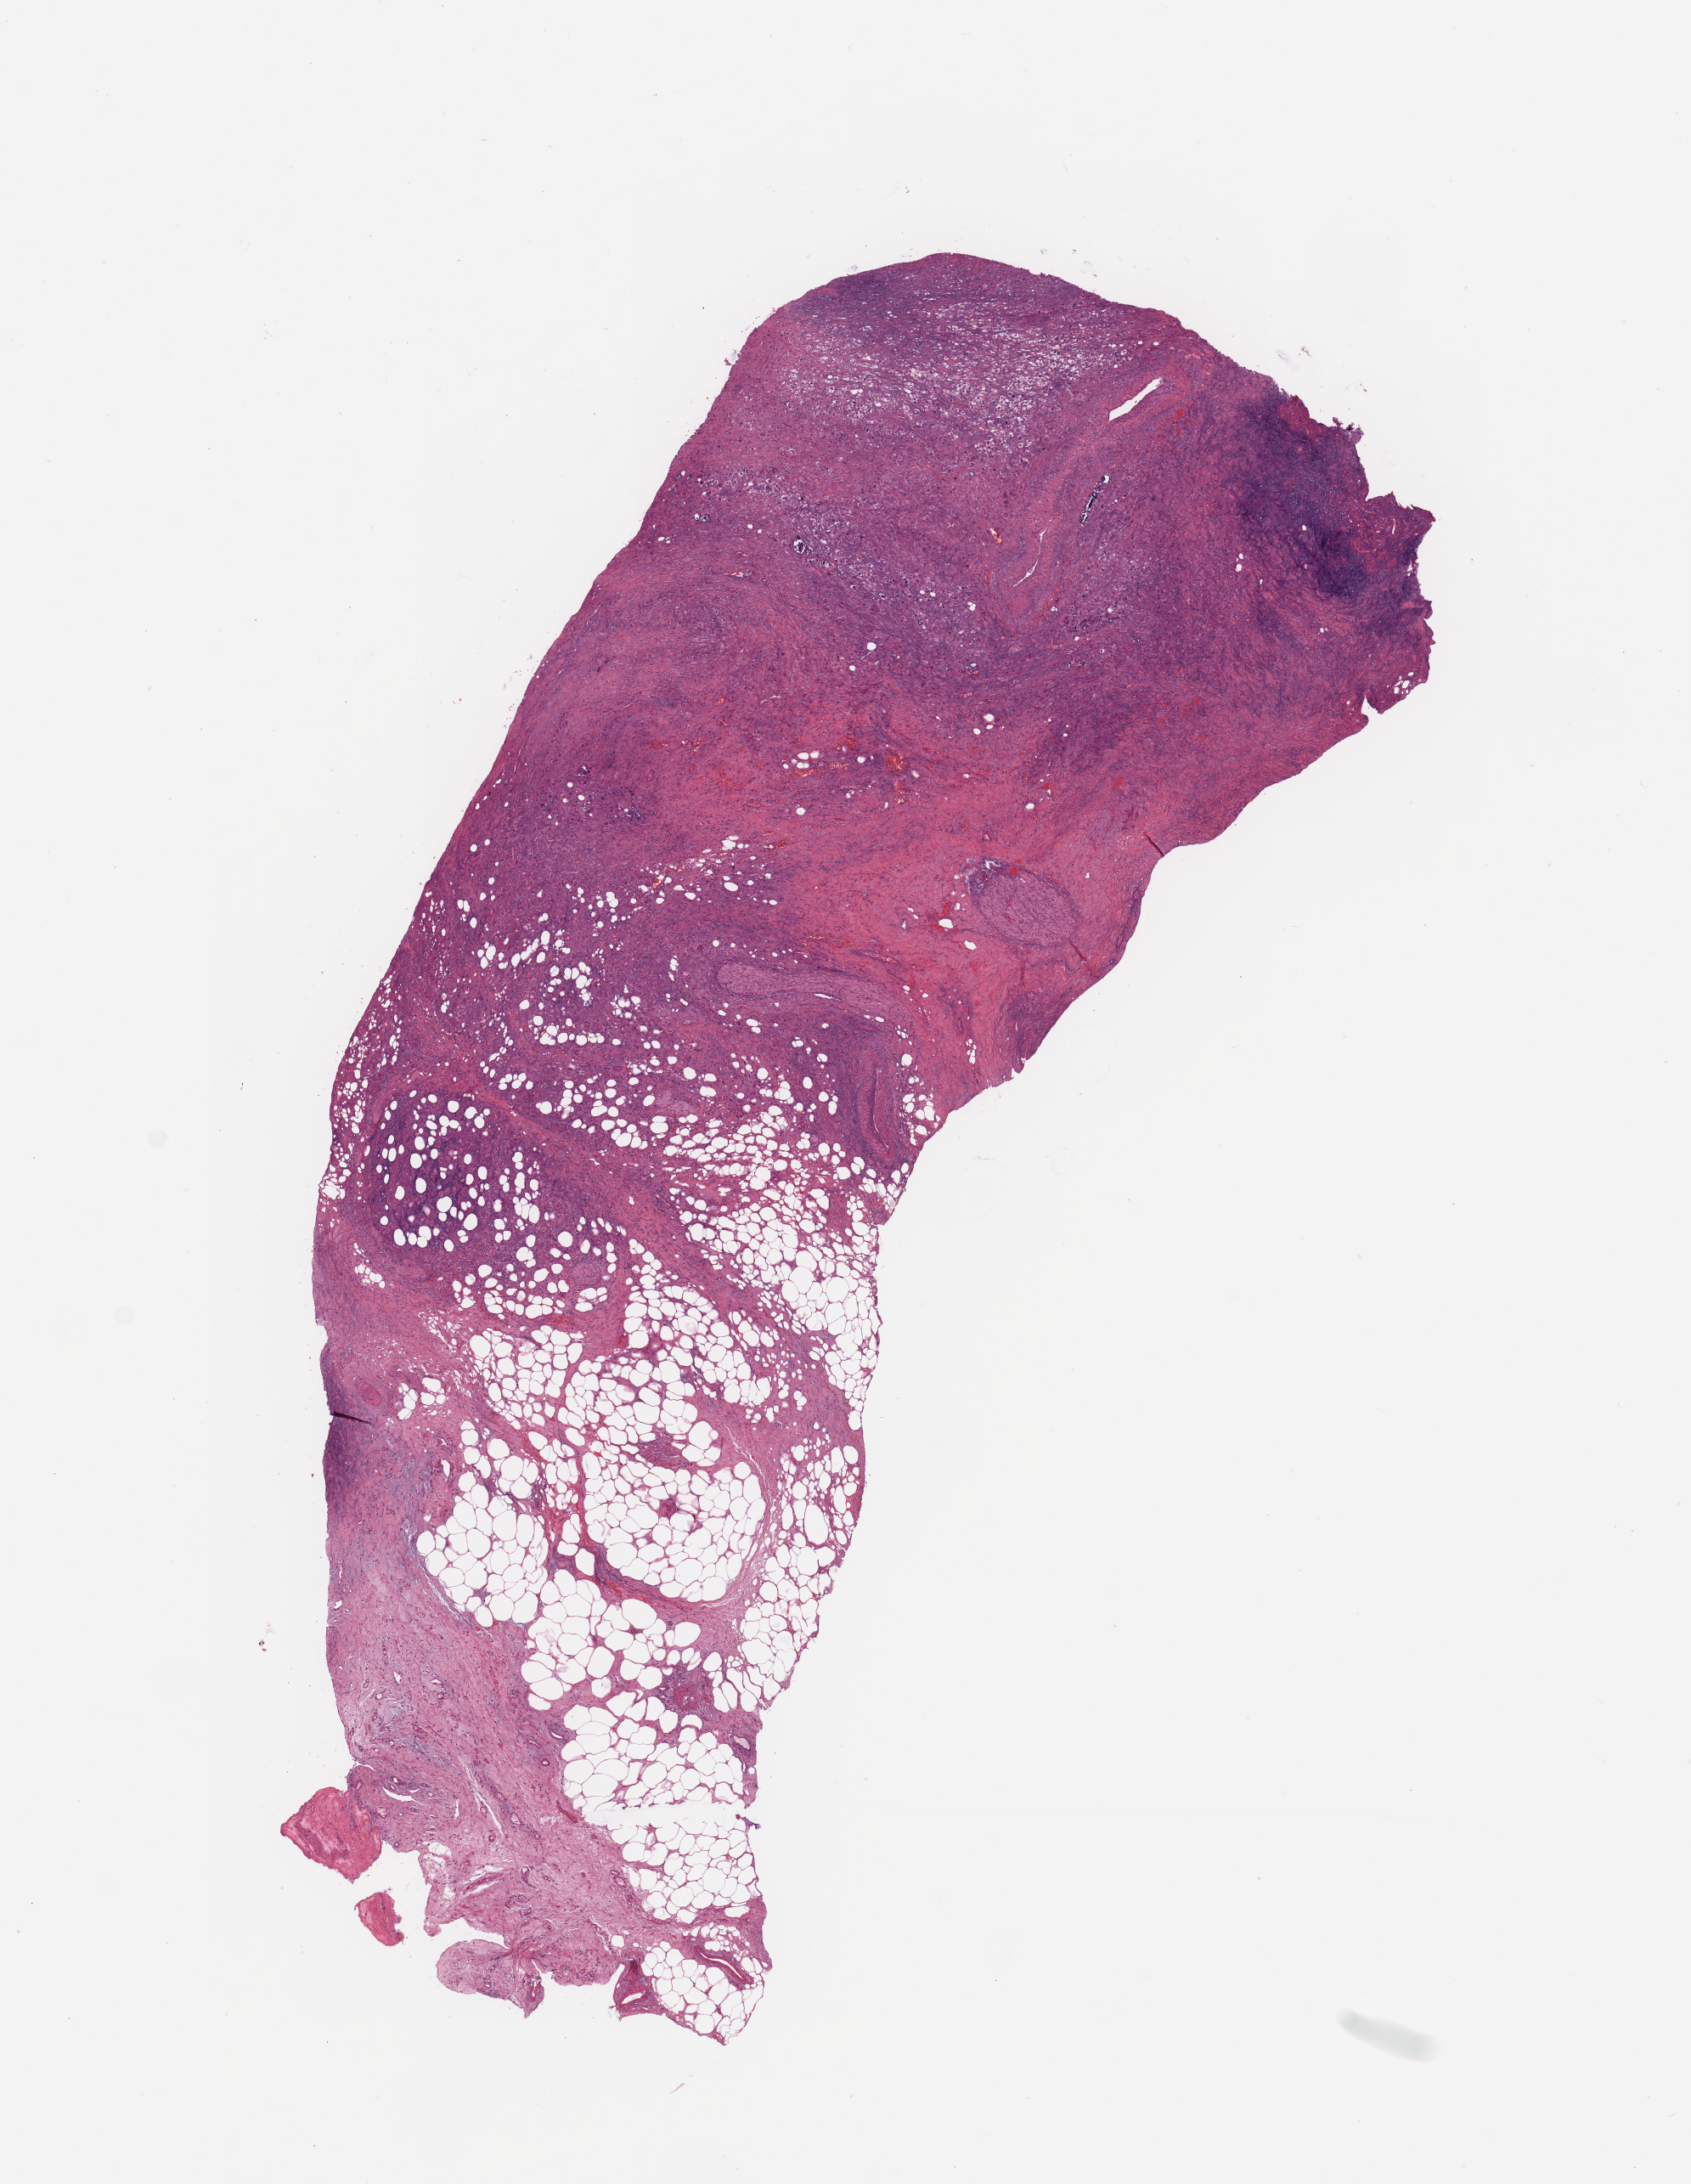
Digitized H&E-stained tissue section (whole slide), whole scanned area (about 7.9 x 10.2 mm) shown as a low-resolution overview. Tumour tissue sample, sampled site: pancreas. Male, 71 y/o. Histologic grade: G3 (poorly differentiated). Pathologist review of this section (percent, as recorded): tumour nuclei 80%, necrosis 0%.
Diagnosis: Infiltrating duct carcinoma, NOS. AJCC pathologic stage: IIB. Primary tumour site (as recorded): head.